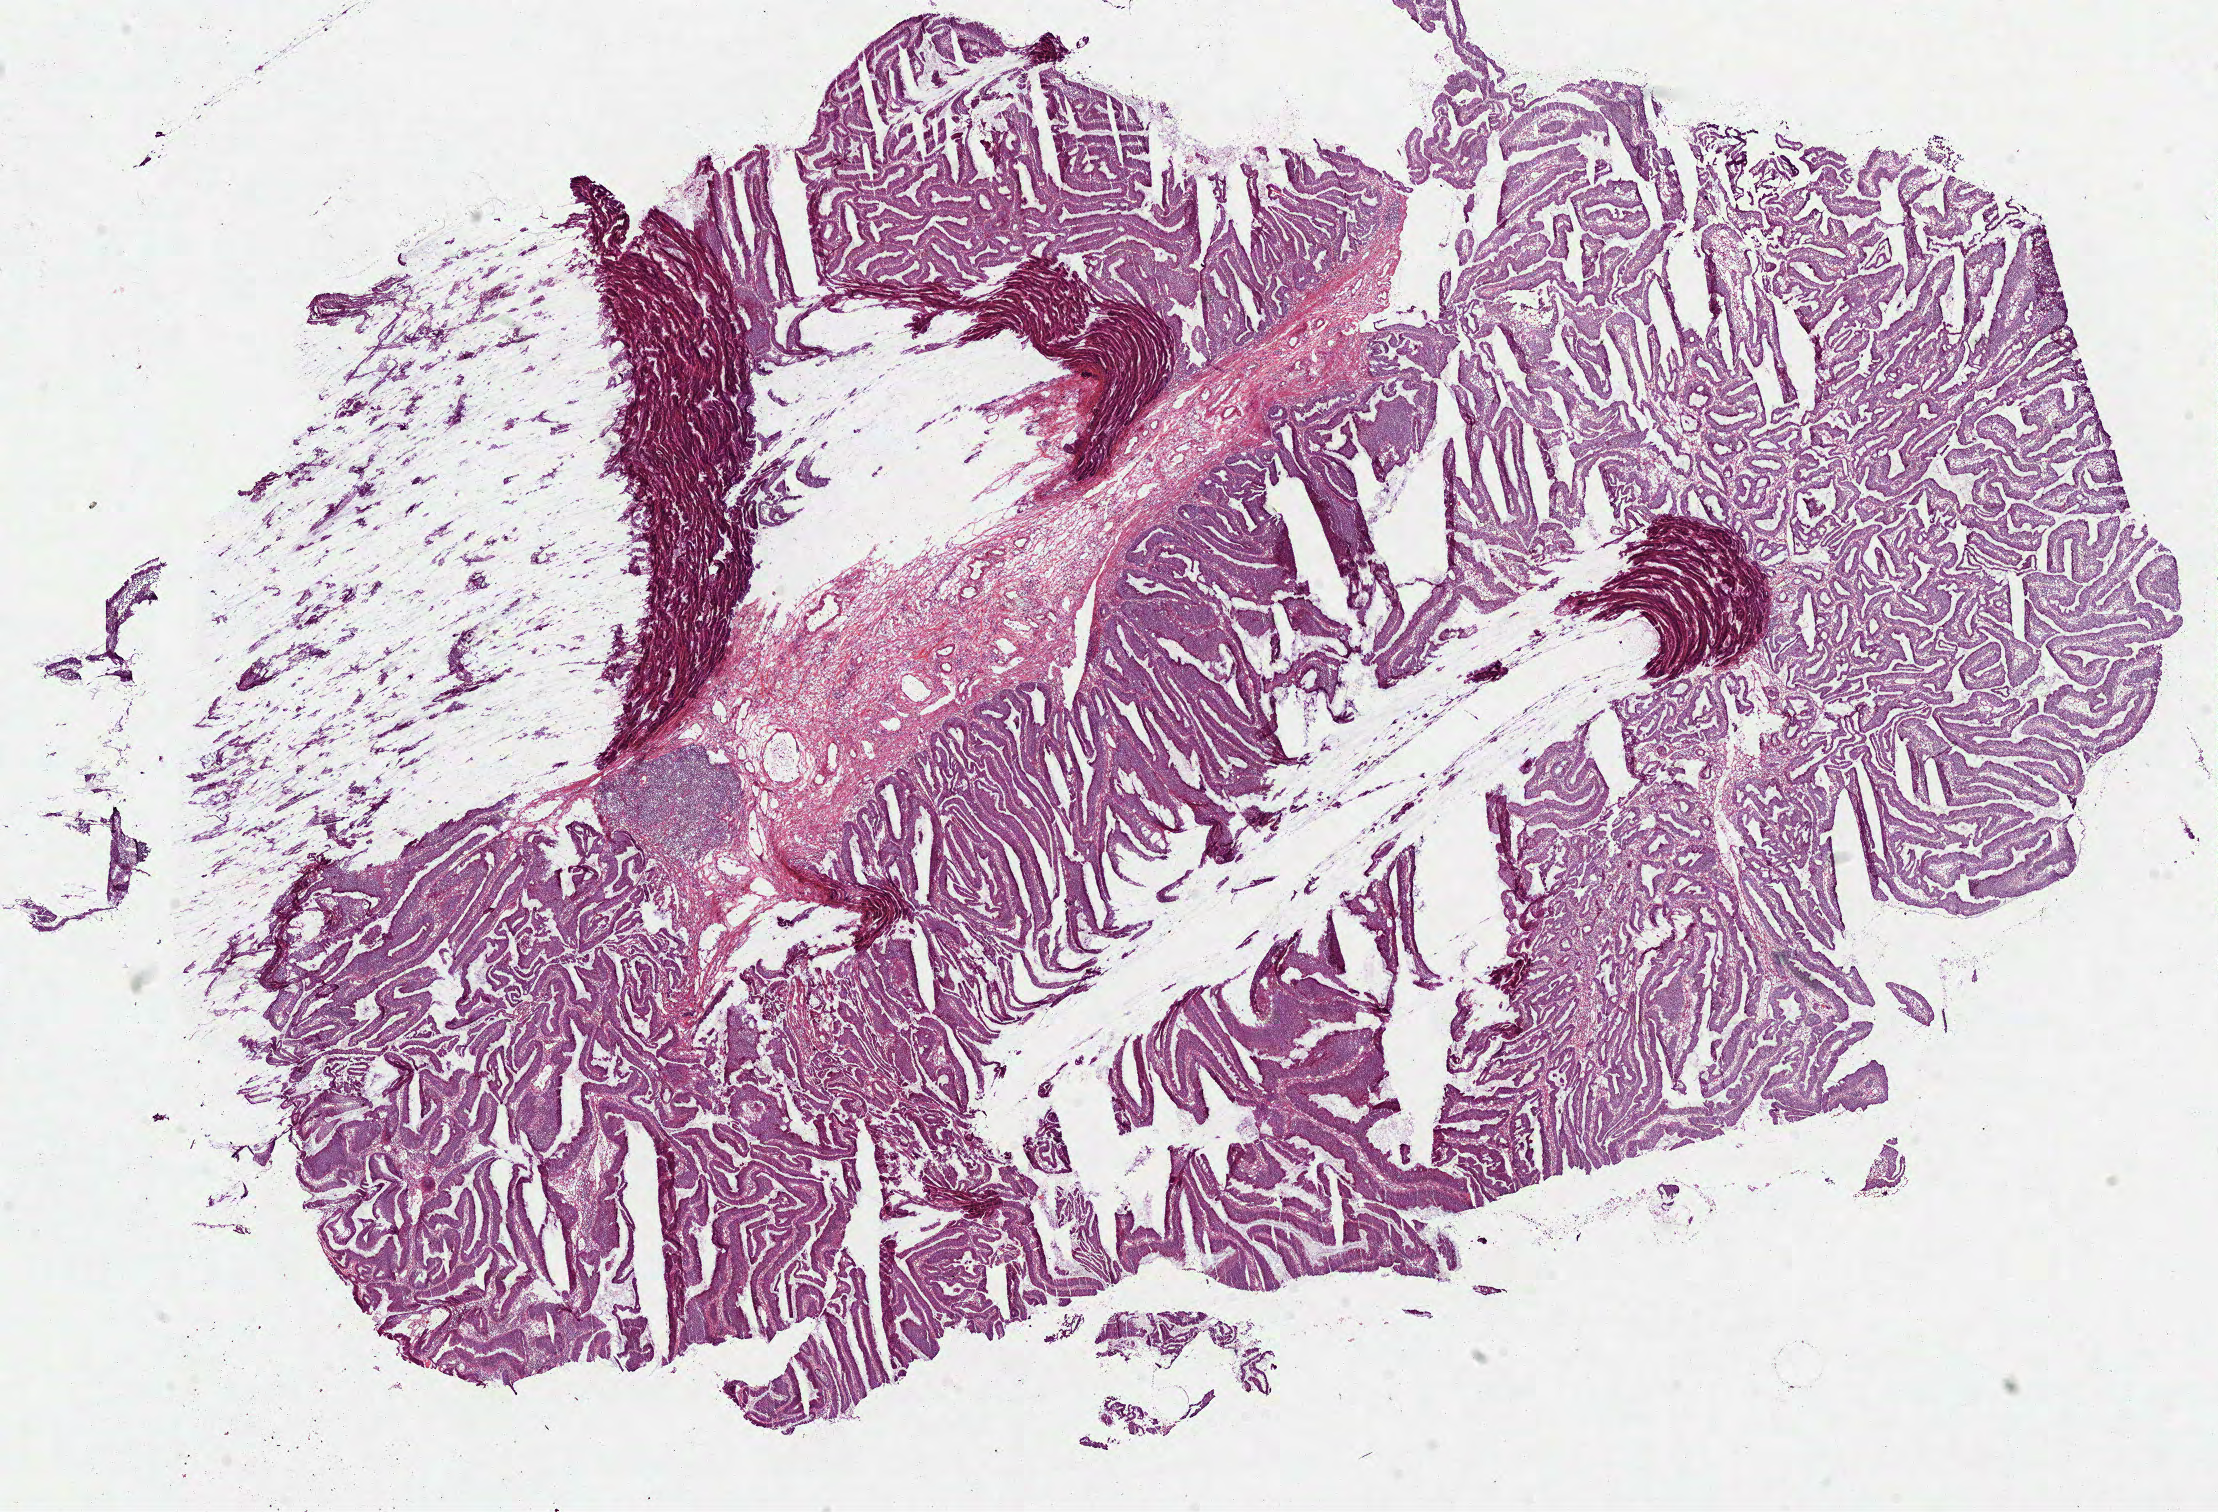
Whole-slide histology image, H&E — low-resolution overview of the scanned area, about 17.9 x 12.2 mm, frozen section from the top of the tissue portion, colon, primary tumour sample. Male, age 72 years at initial diagnosis. Slide review estimates, as recorded: tumour cells 90%, tumour nuclei 80%, normal cells 0%, stromal cells 10%, necrosis 0%.
• AJCC pathologic stage: I (5th edition)
• histologic diagnosis: Adenocarcinoma, NOS (cecum)
• TNM: T2 N0 MX
• lymph nodes positive (case pathology): 0 of 25 examined